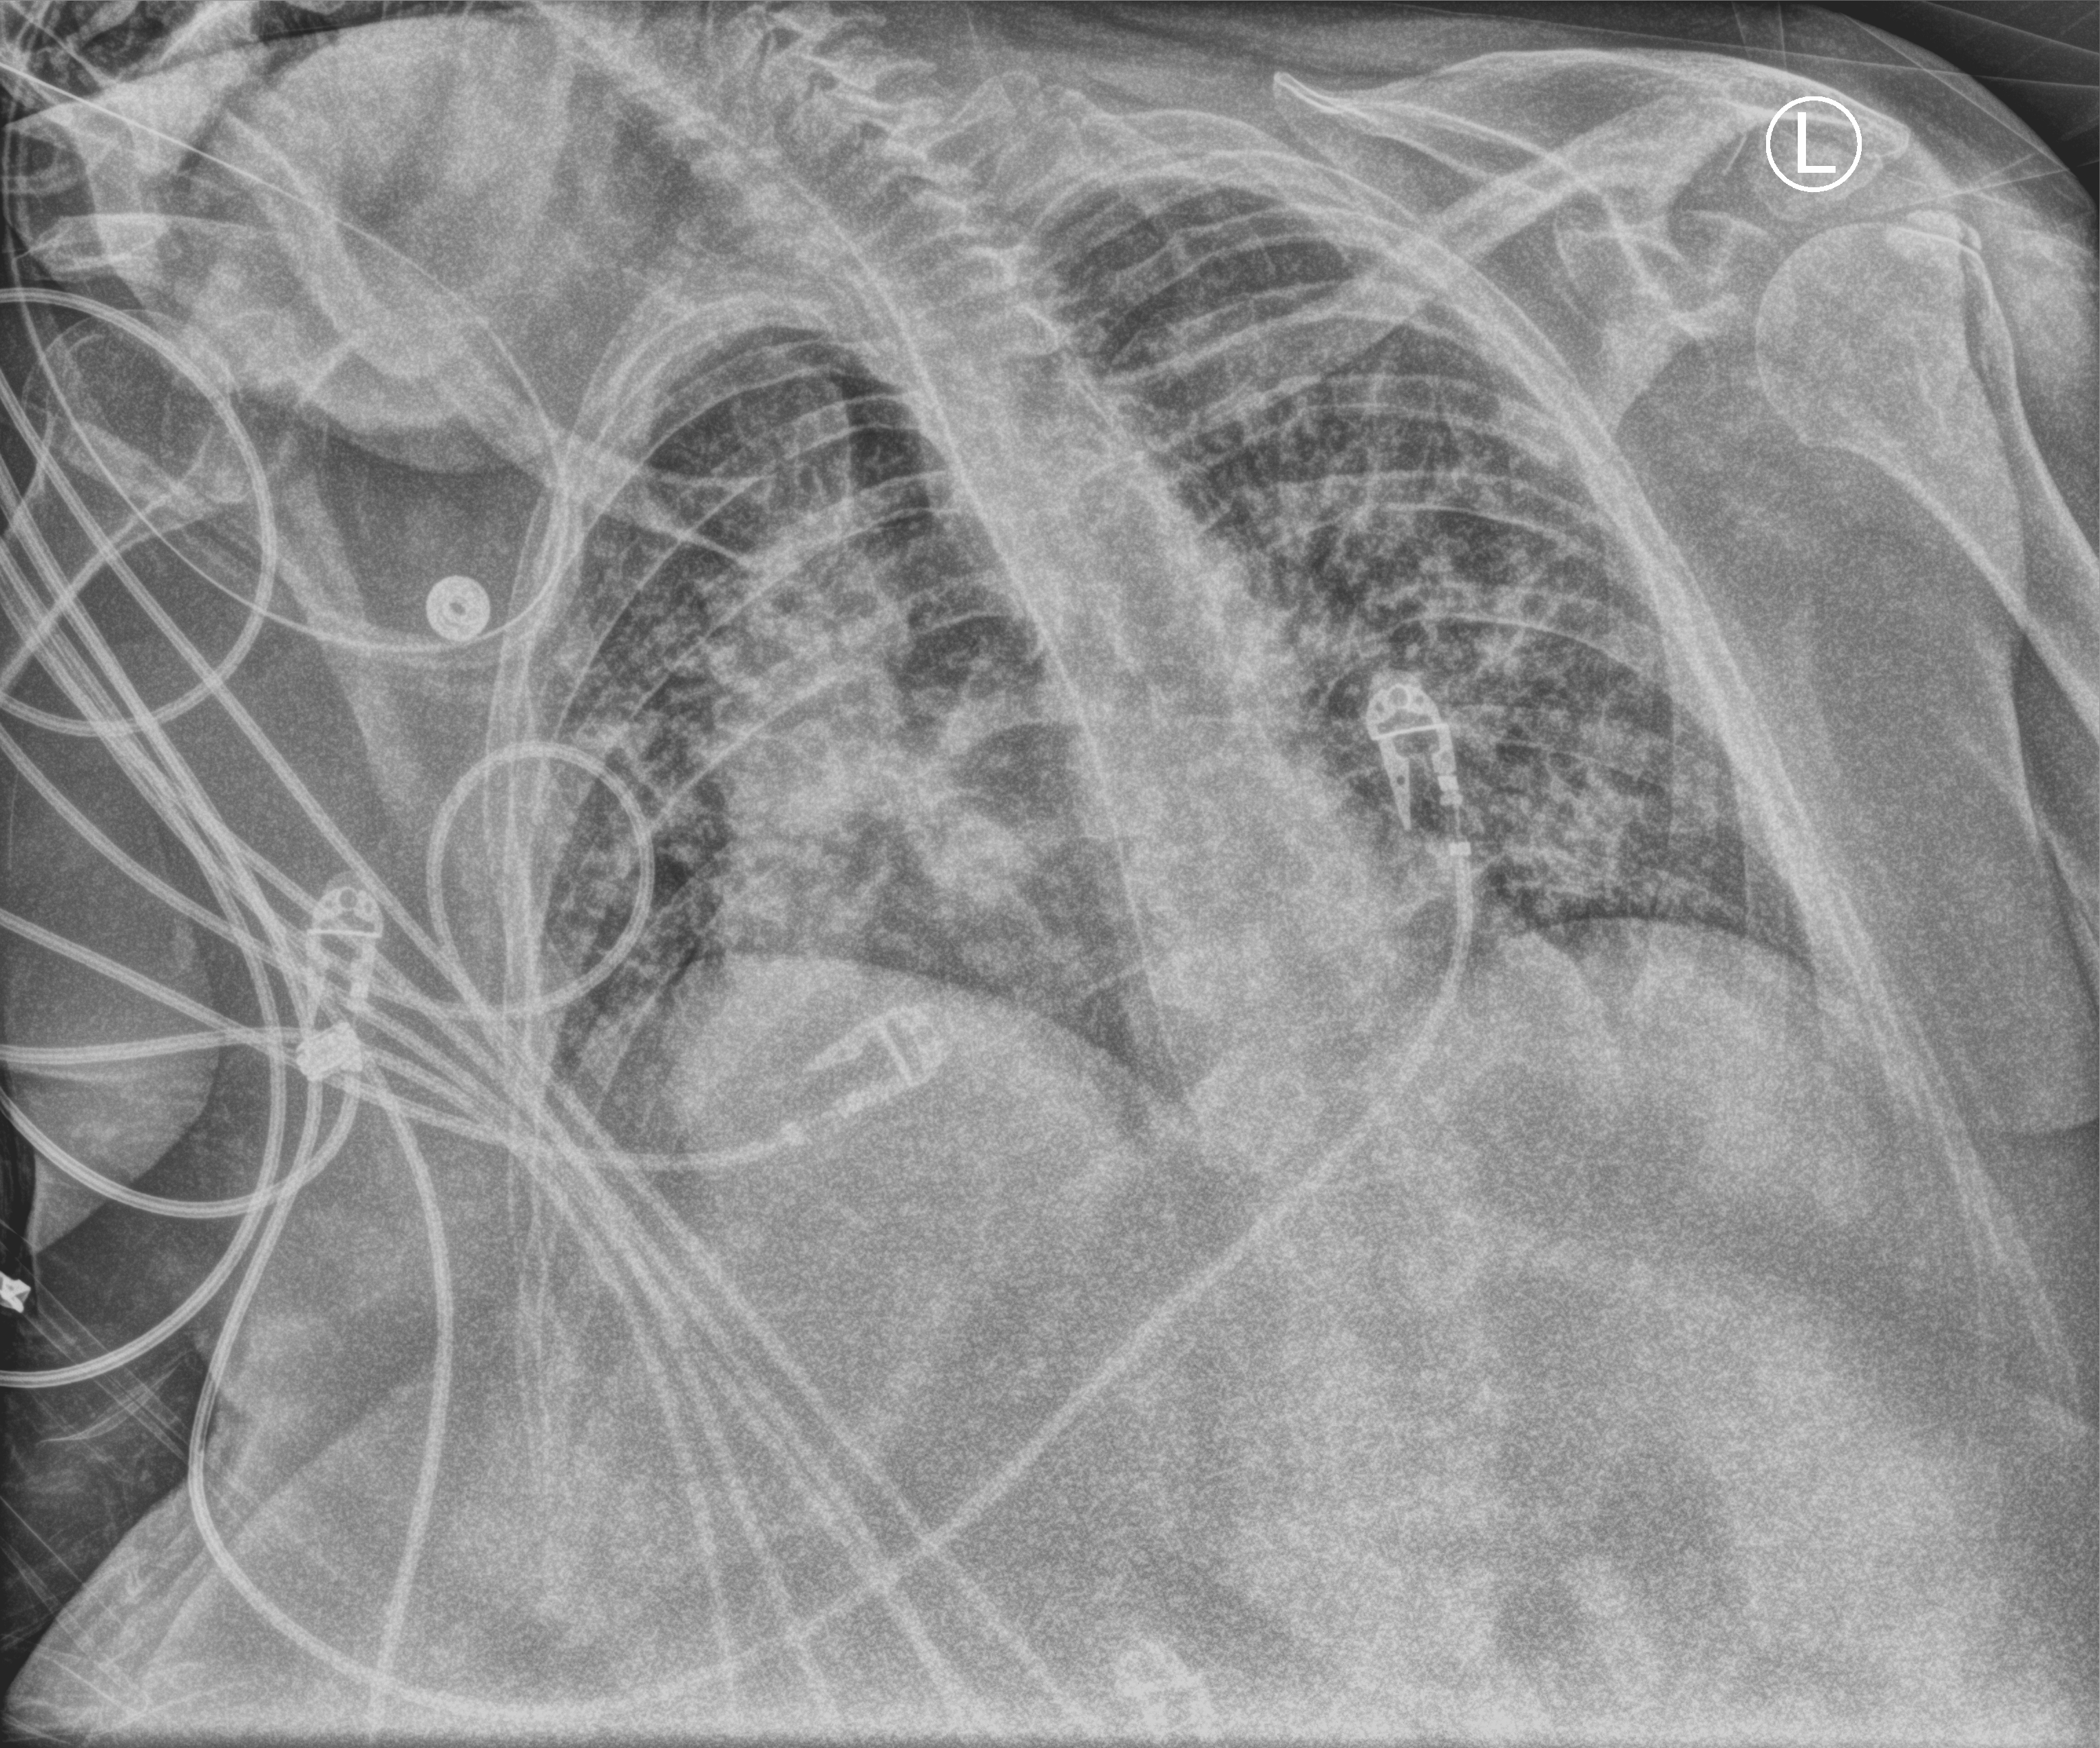
Portable chest radiograph; anteroposterior (AP) projection. Female patient hospitalised with COVID-19, age 75–90 years.
Hospital-stay facts (about this admission, not read from this image; timing relative to this image not recorded):
- mechanically ventilated during this hospital stay: yes
- smoking status (admission record): former